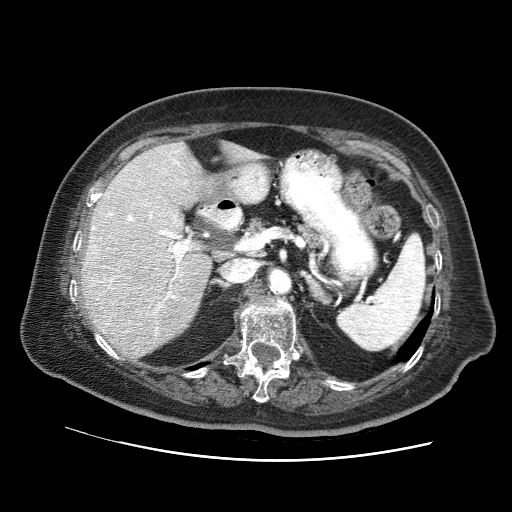
Contrast-enhanced abdominal CT (liver protocol), one axial slice; position 38 of 73 along the scan axis; reconstruction kernel STANDARD; 120 kVp; soft-tissue window (W 400 / L 40 HU); 2.5 mm slice thickness; 512 × 512 image matrix. Case-level facts recorded for this patient, not image findings: diagnosis: hepatocellular carcinoma (patient treated with transarterial chemoembolisation; whether this scan precedes or follows treatment is not stated here); TNM stage (as recorded): Stage-I; Child-Pugh class: A; tumour differentiation: well differentiated.
Annotated regions visible in this slice (semi-automatic segmentation, software-assisted and operator-edited):
- liver parenchyma outside the tumour (the mass and vessels are separate outlines, so this box may not span the whole liver): box from (x=82, y=142) to (x=261, y=356) px
- liver vessels: (x=92, y=150)–(x=259, y=331)